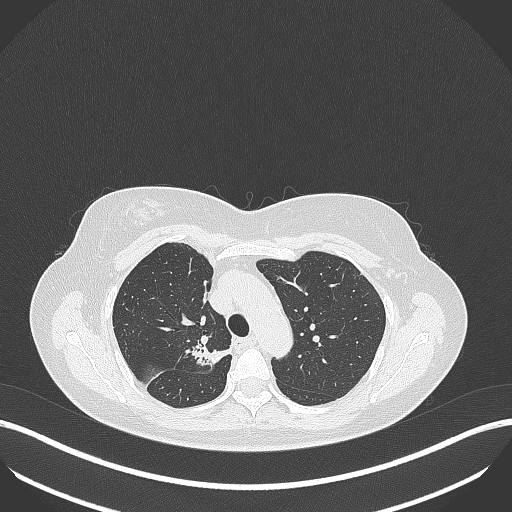
Chest CT, one axial slice. Position 288 of 386 along the scan axis. Lung window (W 1500 / L -600 HU). 512 × 512 image matrix. Female patient, age 65 years. From the clinical record (not read from this slice): clinical TNM (as recorded): T1b N0 M0.
Structures marked on this image (rectangle marked by the reading radiologist):
- lung tumour (recorded histology: adenocarcinoma): bounding box (x1, y1, x2, y2) in pixels: (187, 336, 229, 373)